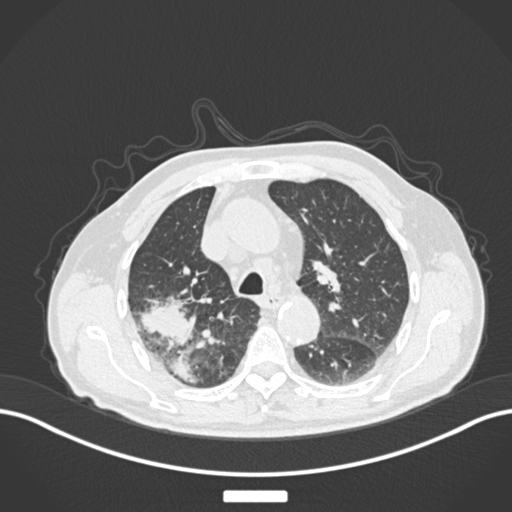
Chest CT, one axial slice. Slice 130 of 201 in the series (ordered by position). Reconstruction kernel B30f. 120 kVp. Lung window (W 1500 / L -600 HU). 512 × 512 image matrix. Patient: male, 72 years. Case-level facts recorded for this patient, not image findings: clinical TNM (as recorded): T3 N2 M0.
Outlined on this slice (bounding box drawn by a radiologist):
- lung tumour (recorded histology: adenocarcinoma): bounding box (x1, y1, x2, y2) in pixels: (138, 292, 199, 350)